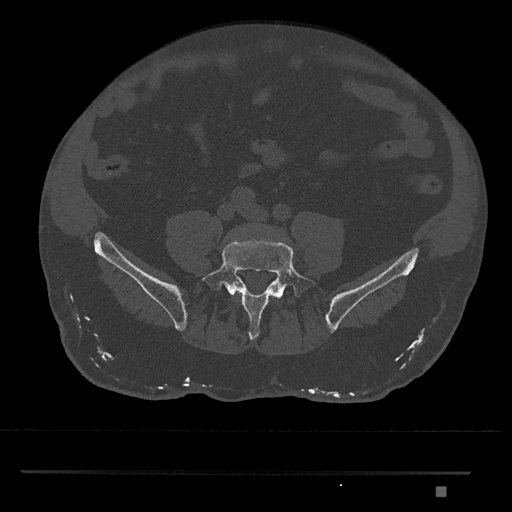
CT including the spine, one axial slice; slice 562 of 1134 in the series (ordered by position); reconstruction kernel Br40s/3; bone window (W 1800 / L 400 HU); 512 × 512 image matrix, field of view 429 × 429 mm. Male patient, age 65 years. Case-level facts recorded for this patient, not image findings: primary cancer: prostate.
Annotated regions visible in this slice (semi-automatic segmentation, software-assisted and operator-edited):
- L4 vertebra: bounding box [x1, y1, x2, y2] px = [233, 291, 238, 296]
- L5 vertebra: [201, 240, 317, 340]